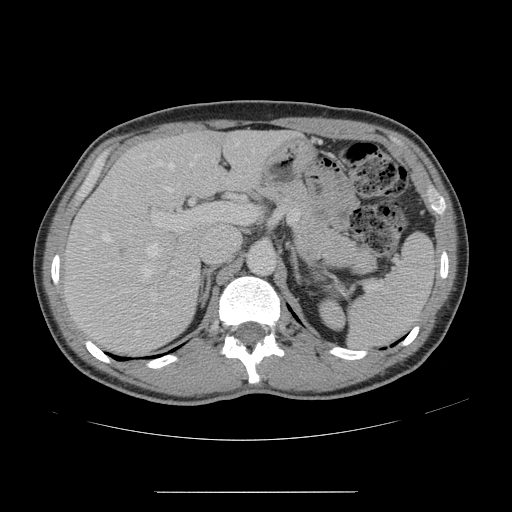
Contrast-enhanced abdominal CT, one axial slice. Slice 93 of 178 in the series (ordered by position). 120 kVp. Intravenous contrast given. Soft-tissue window (W 400 / L 40 HU). 512 × 512 image matrix. Male patient, age 53 years. From the clinical record (not read from this slice): diagnosis: colorectal cancer liver metastases, imaged before liver resection; multiple liver metastases: yes; largest metastasis: 2.4 cm; disease in both lobes: no.
Annotated regions visible in this slice (outlined manually by an expert reader):
- hepatic veins: bounding box <102,154,197,280> (left, top, right, bottom; pixels)
- liver: <67,131,287,352>
- planned liver remnant (the part of the liver to remain after resection): <148,131,287,193>
- portal vein (with intrahepatic branches): <152,204,256,274>